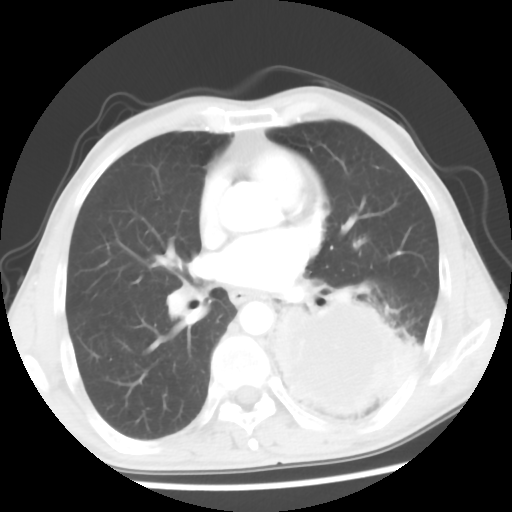
Chest CT, one axial slice. Reconstruction kernel STANDARD. 120 kVp. Lung window (W 1500 / L -600 HU). 512 × 512 image matrix, field of view 318 × 318 mm. Patient: male, 60 years. Case-level facts recorded for this patient, not image findings: clinical TNM (as recorded): T4 N0 M0.
Structures marked on this image (rectangle marked by the reading radiologist):
- lung tumour (recorded histology: squamous cell carcinoma): bounding box (x1, y1, x2, y2) in pixels: (265, 293, 423, 420)